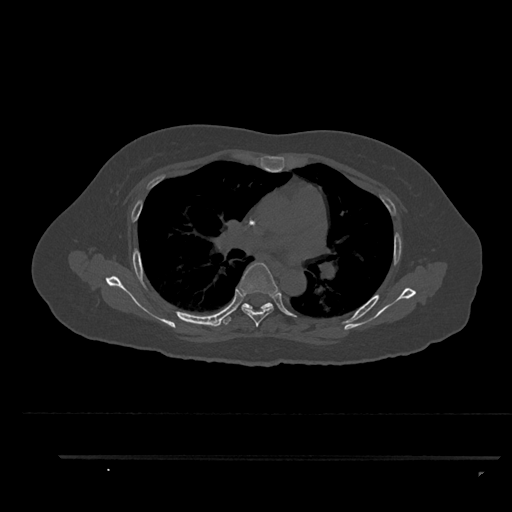
CT including the spine, one axial slice; position 586 of 797 along the scan axis; 120 kVp; bone window (W 1800 / L 400 HU); 0.5 mm slice thickness; 512 × 512 image matrix, field of view 408 × 408 mm. Female patient, age 44 years. From the clinical record (not read from this slice): primary cancer: renal.
Annotated regions visible in this slice (semi-automatic segmentation, software-assisted and operator-edited):
- T5 vertebra: bounding box <239,262,278,327> (left, top, right, bottom; pixels)
- T6 vertebra: <224,302,273,325>